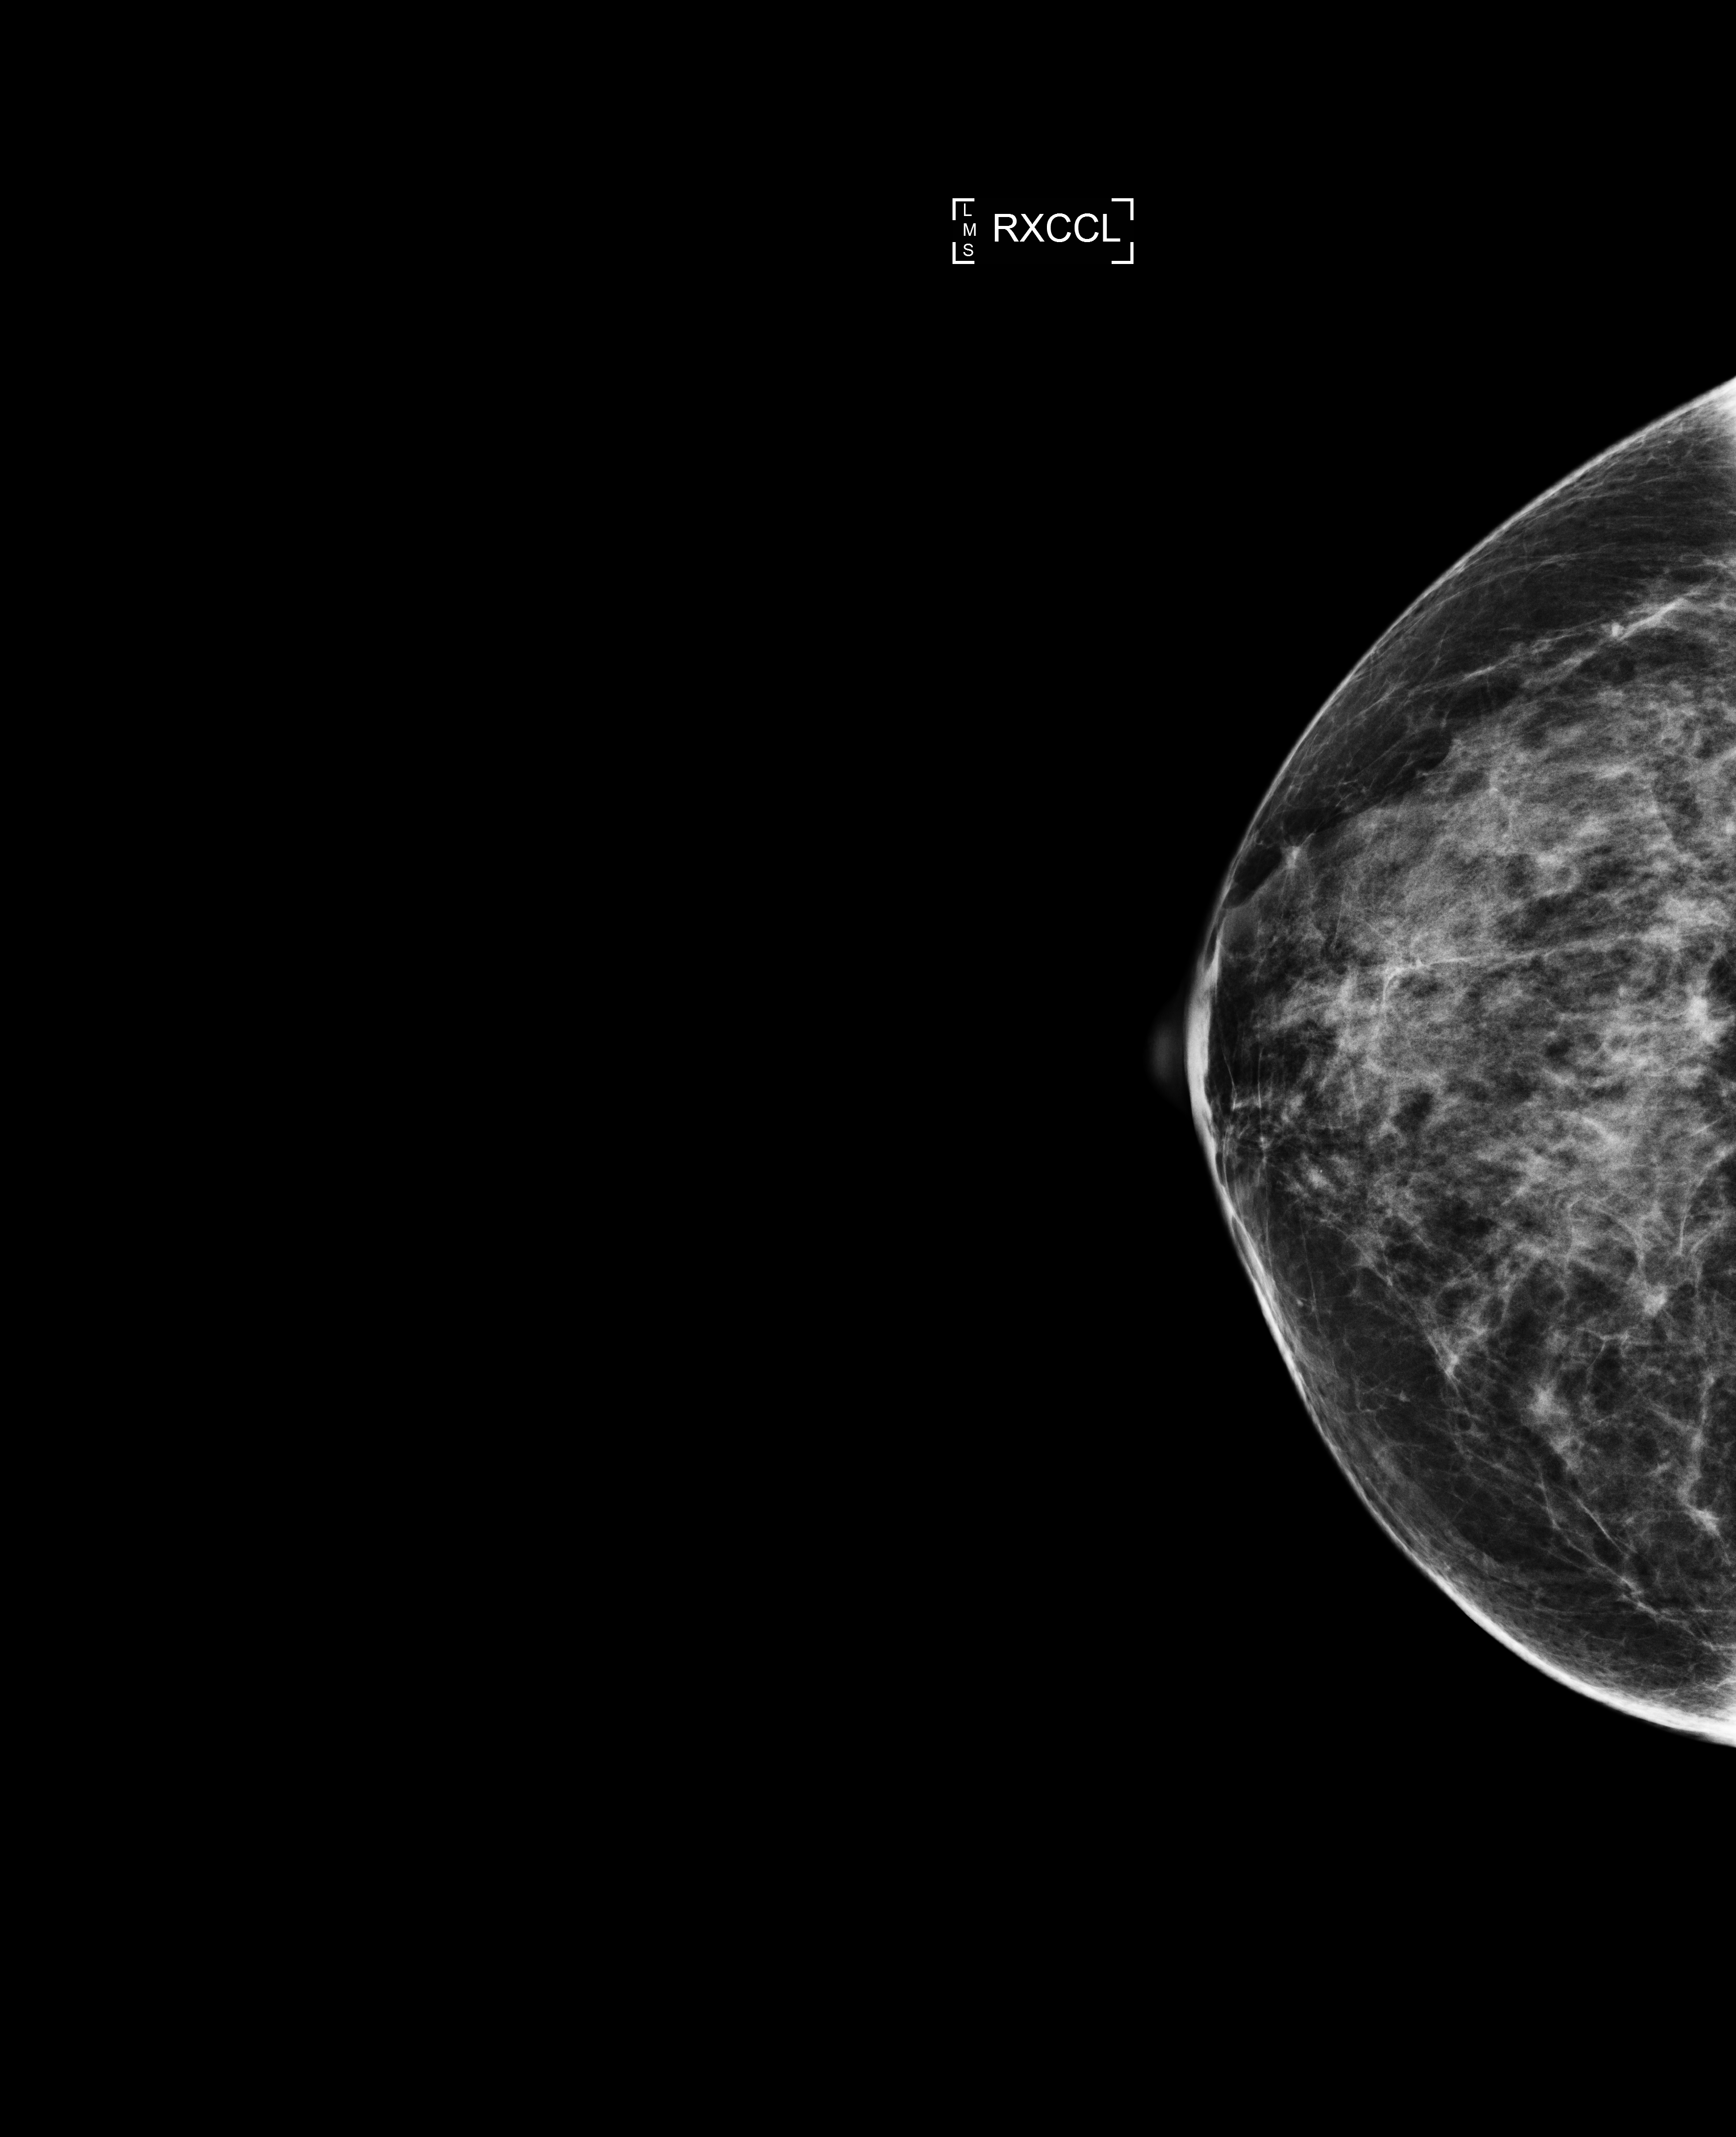
Digital mammogram (FFDM); right breast; exaggerated CC view (lateral); screening examination; compressed breast thickness 52 mm. Female patient, age 59 years.
Breast density at the screening exam (both breasts): heterogeneously dense (BI-RADS density category c). Final BI-RADS assessment for this screening round (tomosynthesis exam, both breasts): category 1. Recall: no recall after this screen.